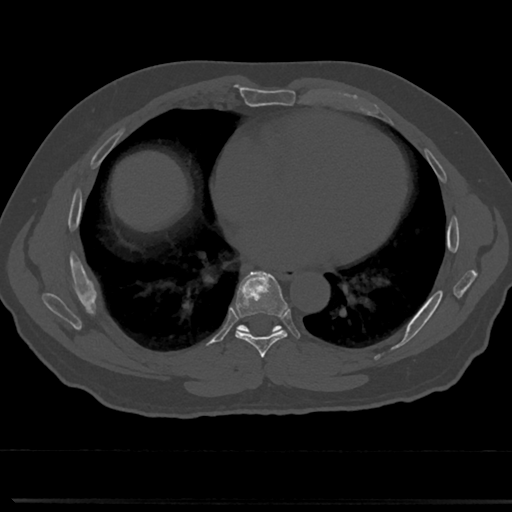
CT including the spine, one axial slice; slice 392 of 817 in the series (ordered by position); bone window (W 1800 / L 400 HU); 0.5 mm slice thickness; 512 × 512 image matrix, field of view 355 × 355 mm. Patient: male, 61 years. Case-level facts recorded for this patient, not image findings: primary cancer: prostate.
Outlined on this slice (semi-automatic segmentation, software-assisted and operator-edited):
- T6 vertebra: box from (x=260, y=358) to (x=269, y=377) px
- T7 vertebra: (x=214, y=275)–(x=310, y=357)